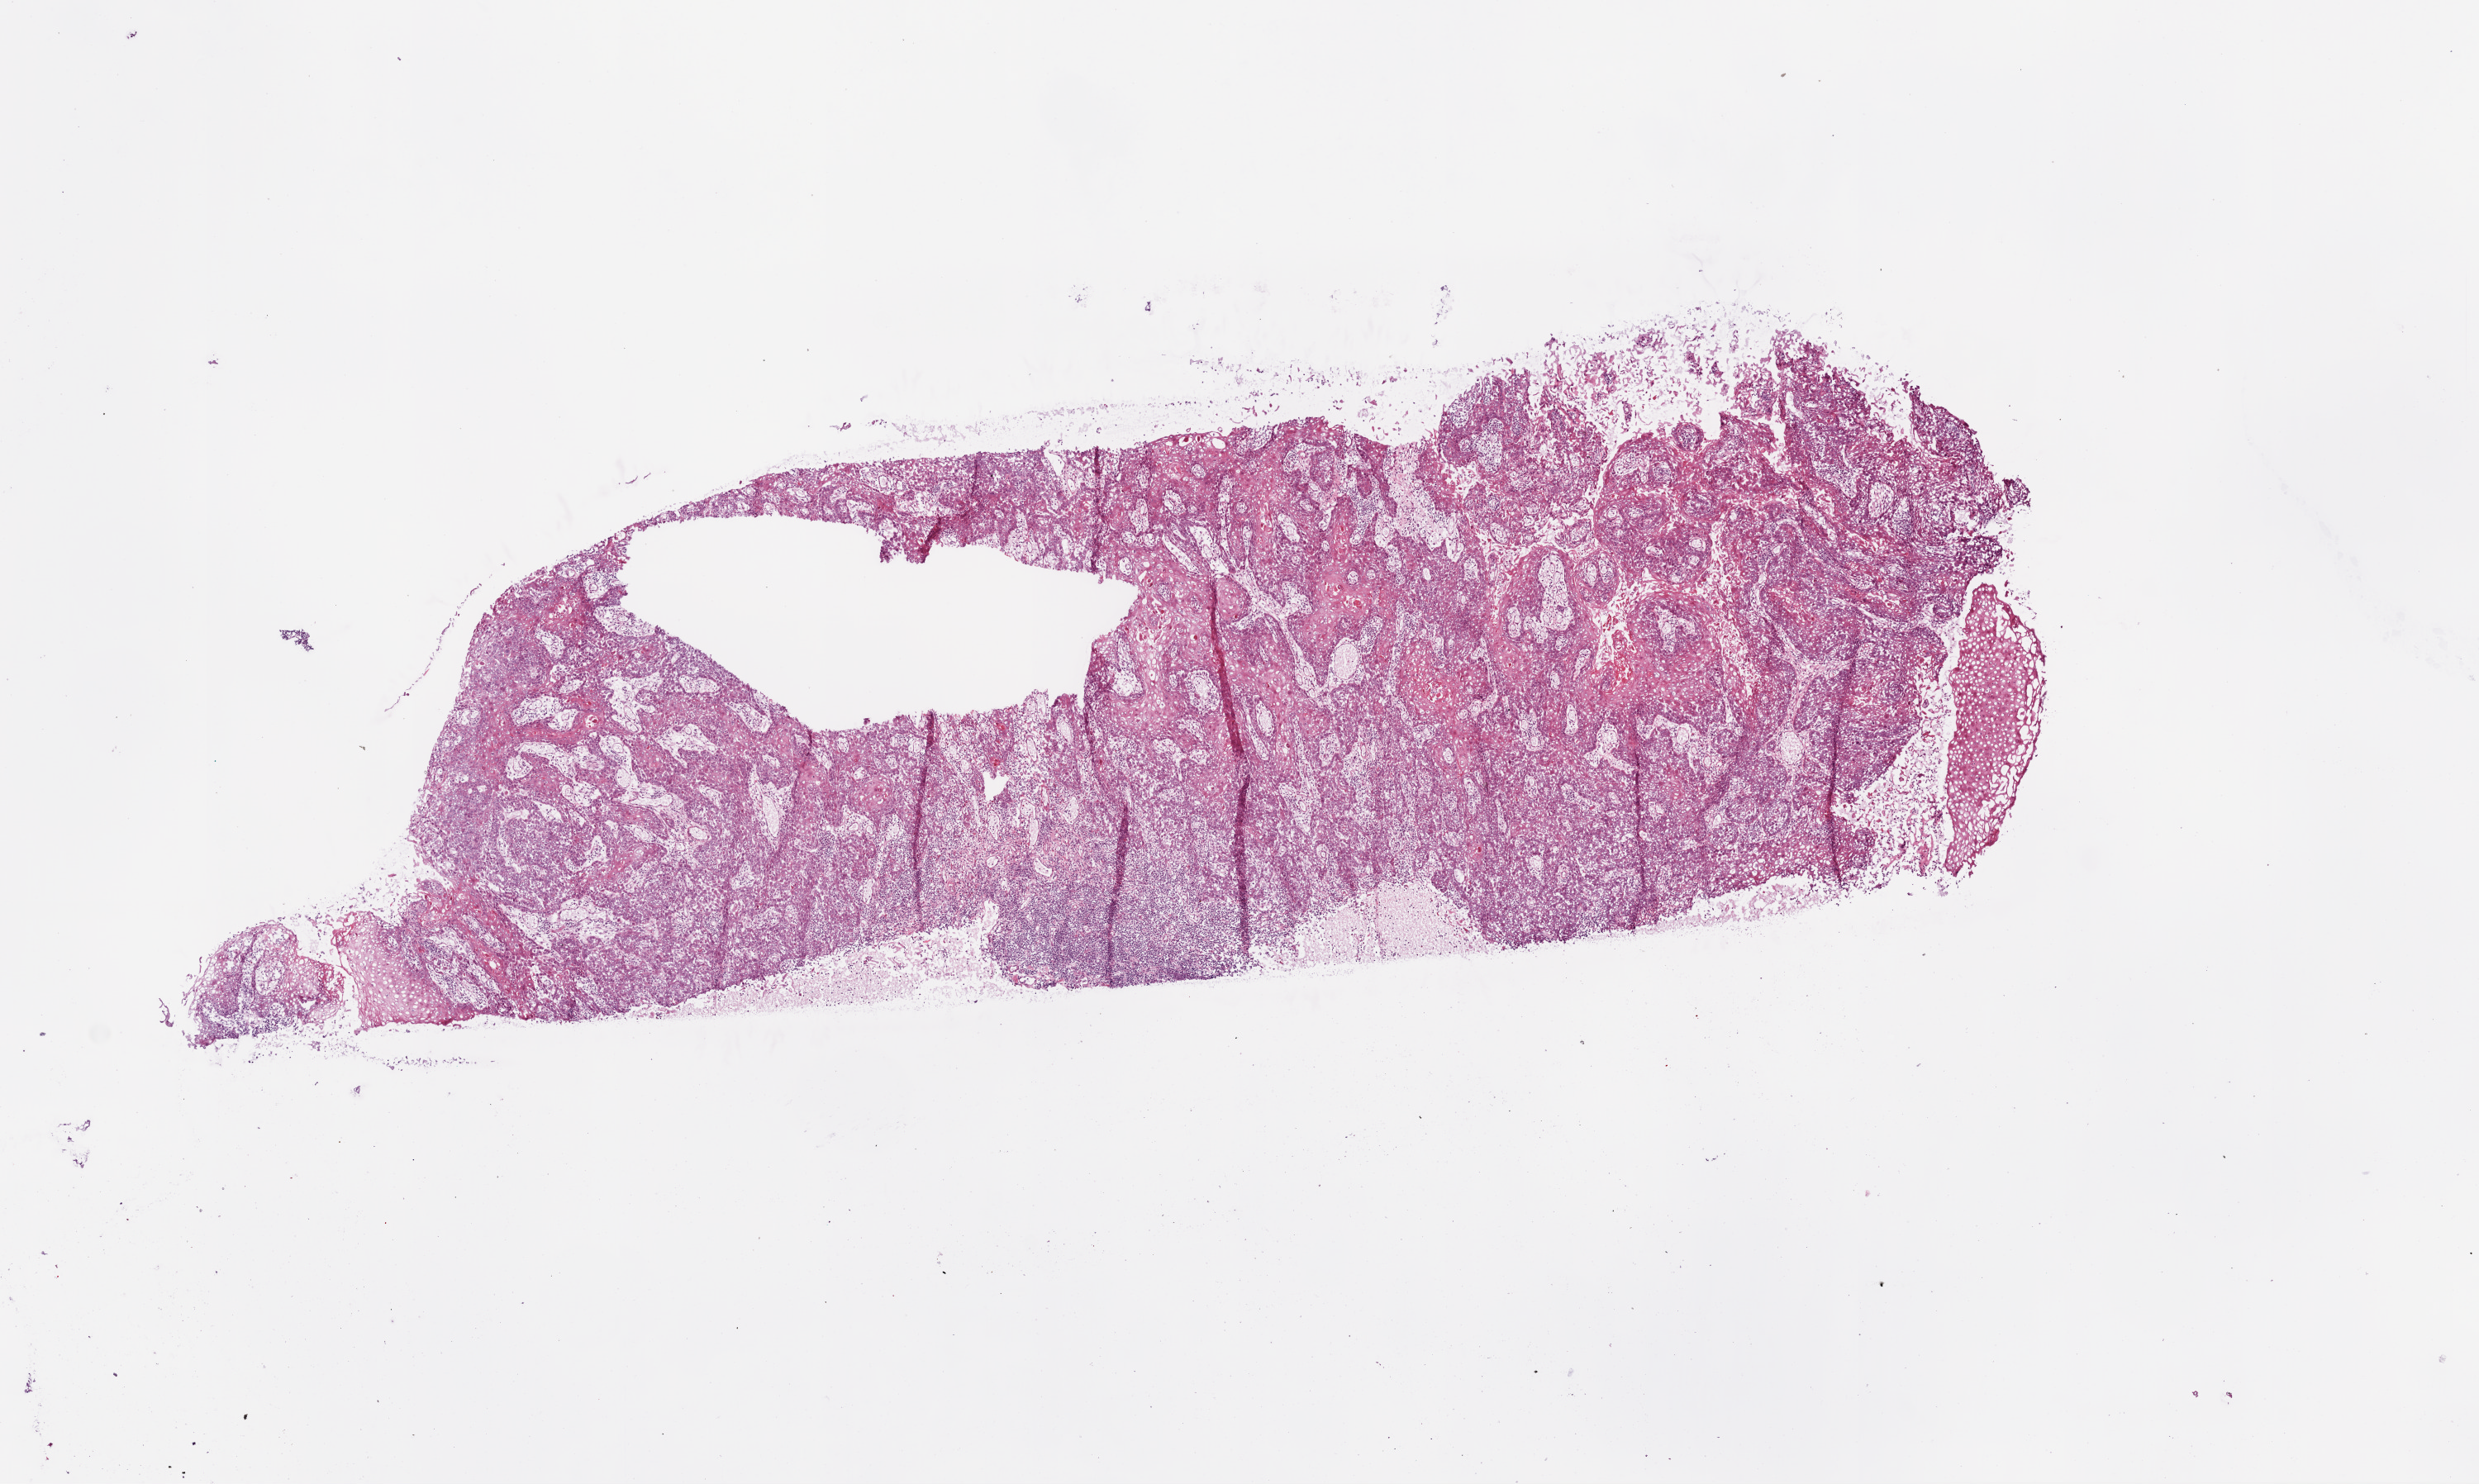
Digitized H&E tissue section (whole slide), low-resolution overview of the scanned area, about 12.0 x 7.2 mm; frozen section; primary tumour sample from the head and neck. Patient: male, age at initial diagnosis 56 years. Histologic grade: G2 (moderately differentiated). Composition of this section per pathologist review: tumour cells 80%, tumour nuclei 60%, normal cells 5%, stromal cells 15%, necrosis 0%.
• AJCC pathologic stage: IVA
• pathologic diagnosis: Squamous cell carcinoma, NOS (overlapping lesion of lip, oral cavity and pharynx)